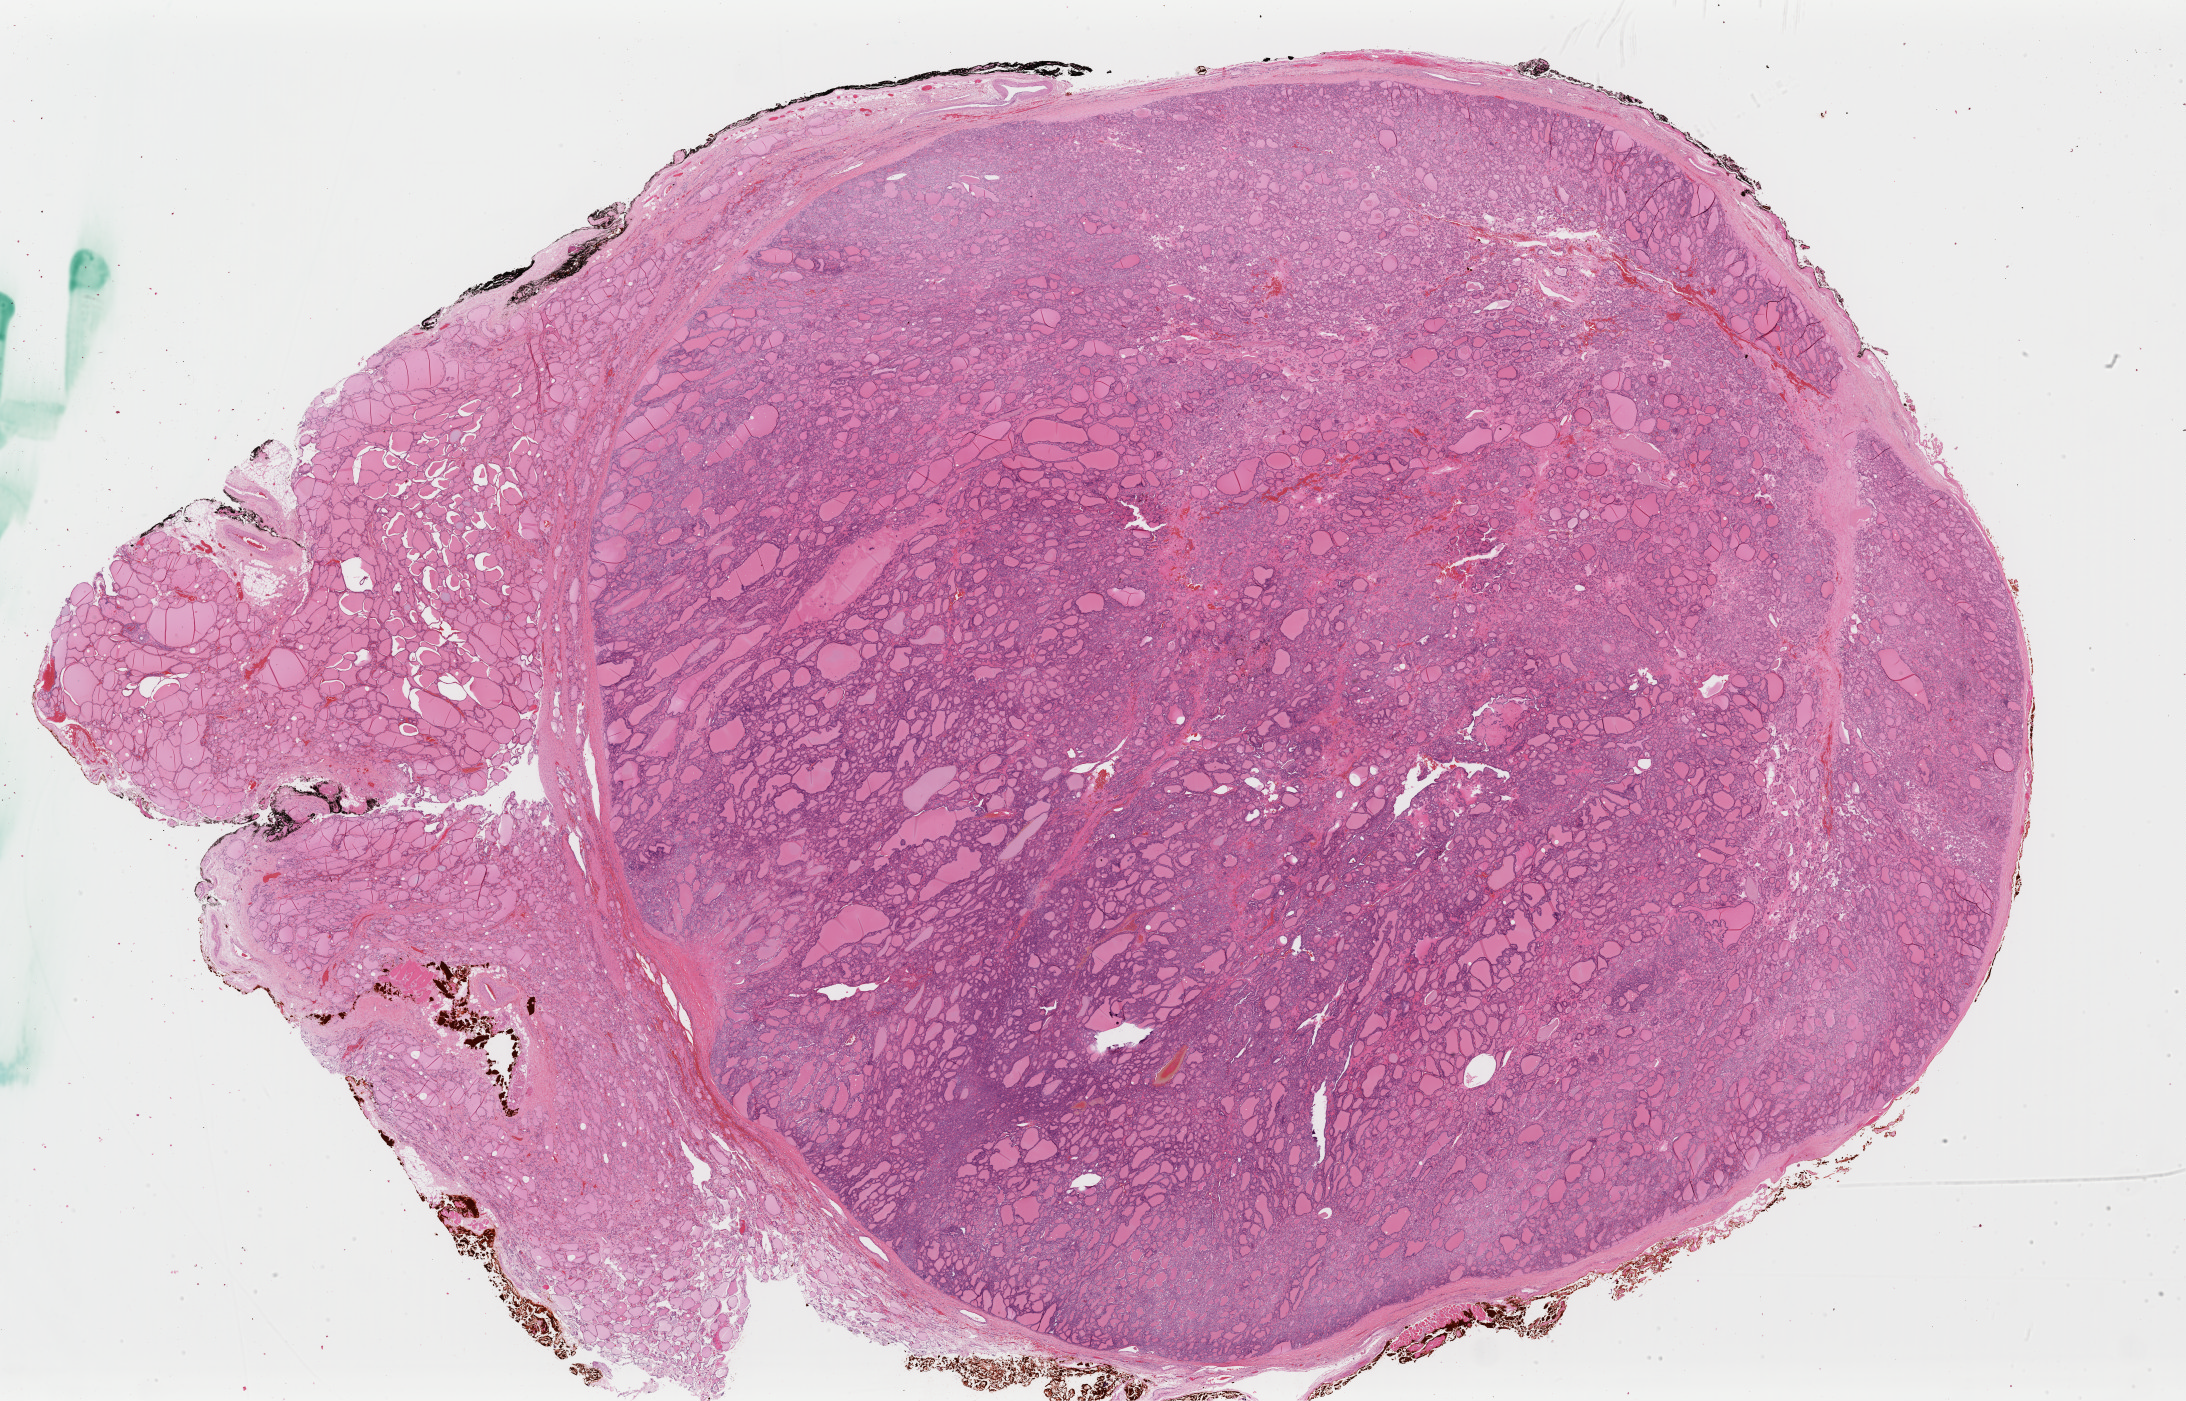
Hematoxylin and eosin (H&E) stained whole-slide image, low-resolution overview of the scanned area, about 34.5 x 22.1 mm (acquisition: 40x scan). FFPE section. Sample: primary tumour, thyroid. Patient: female, age at initial diagnosis 34 years.
- diagnosis: Papillary carcinoma, follicular variant (thyroid gland)
- AJCC pathologic stage: I